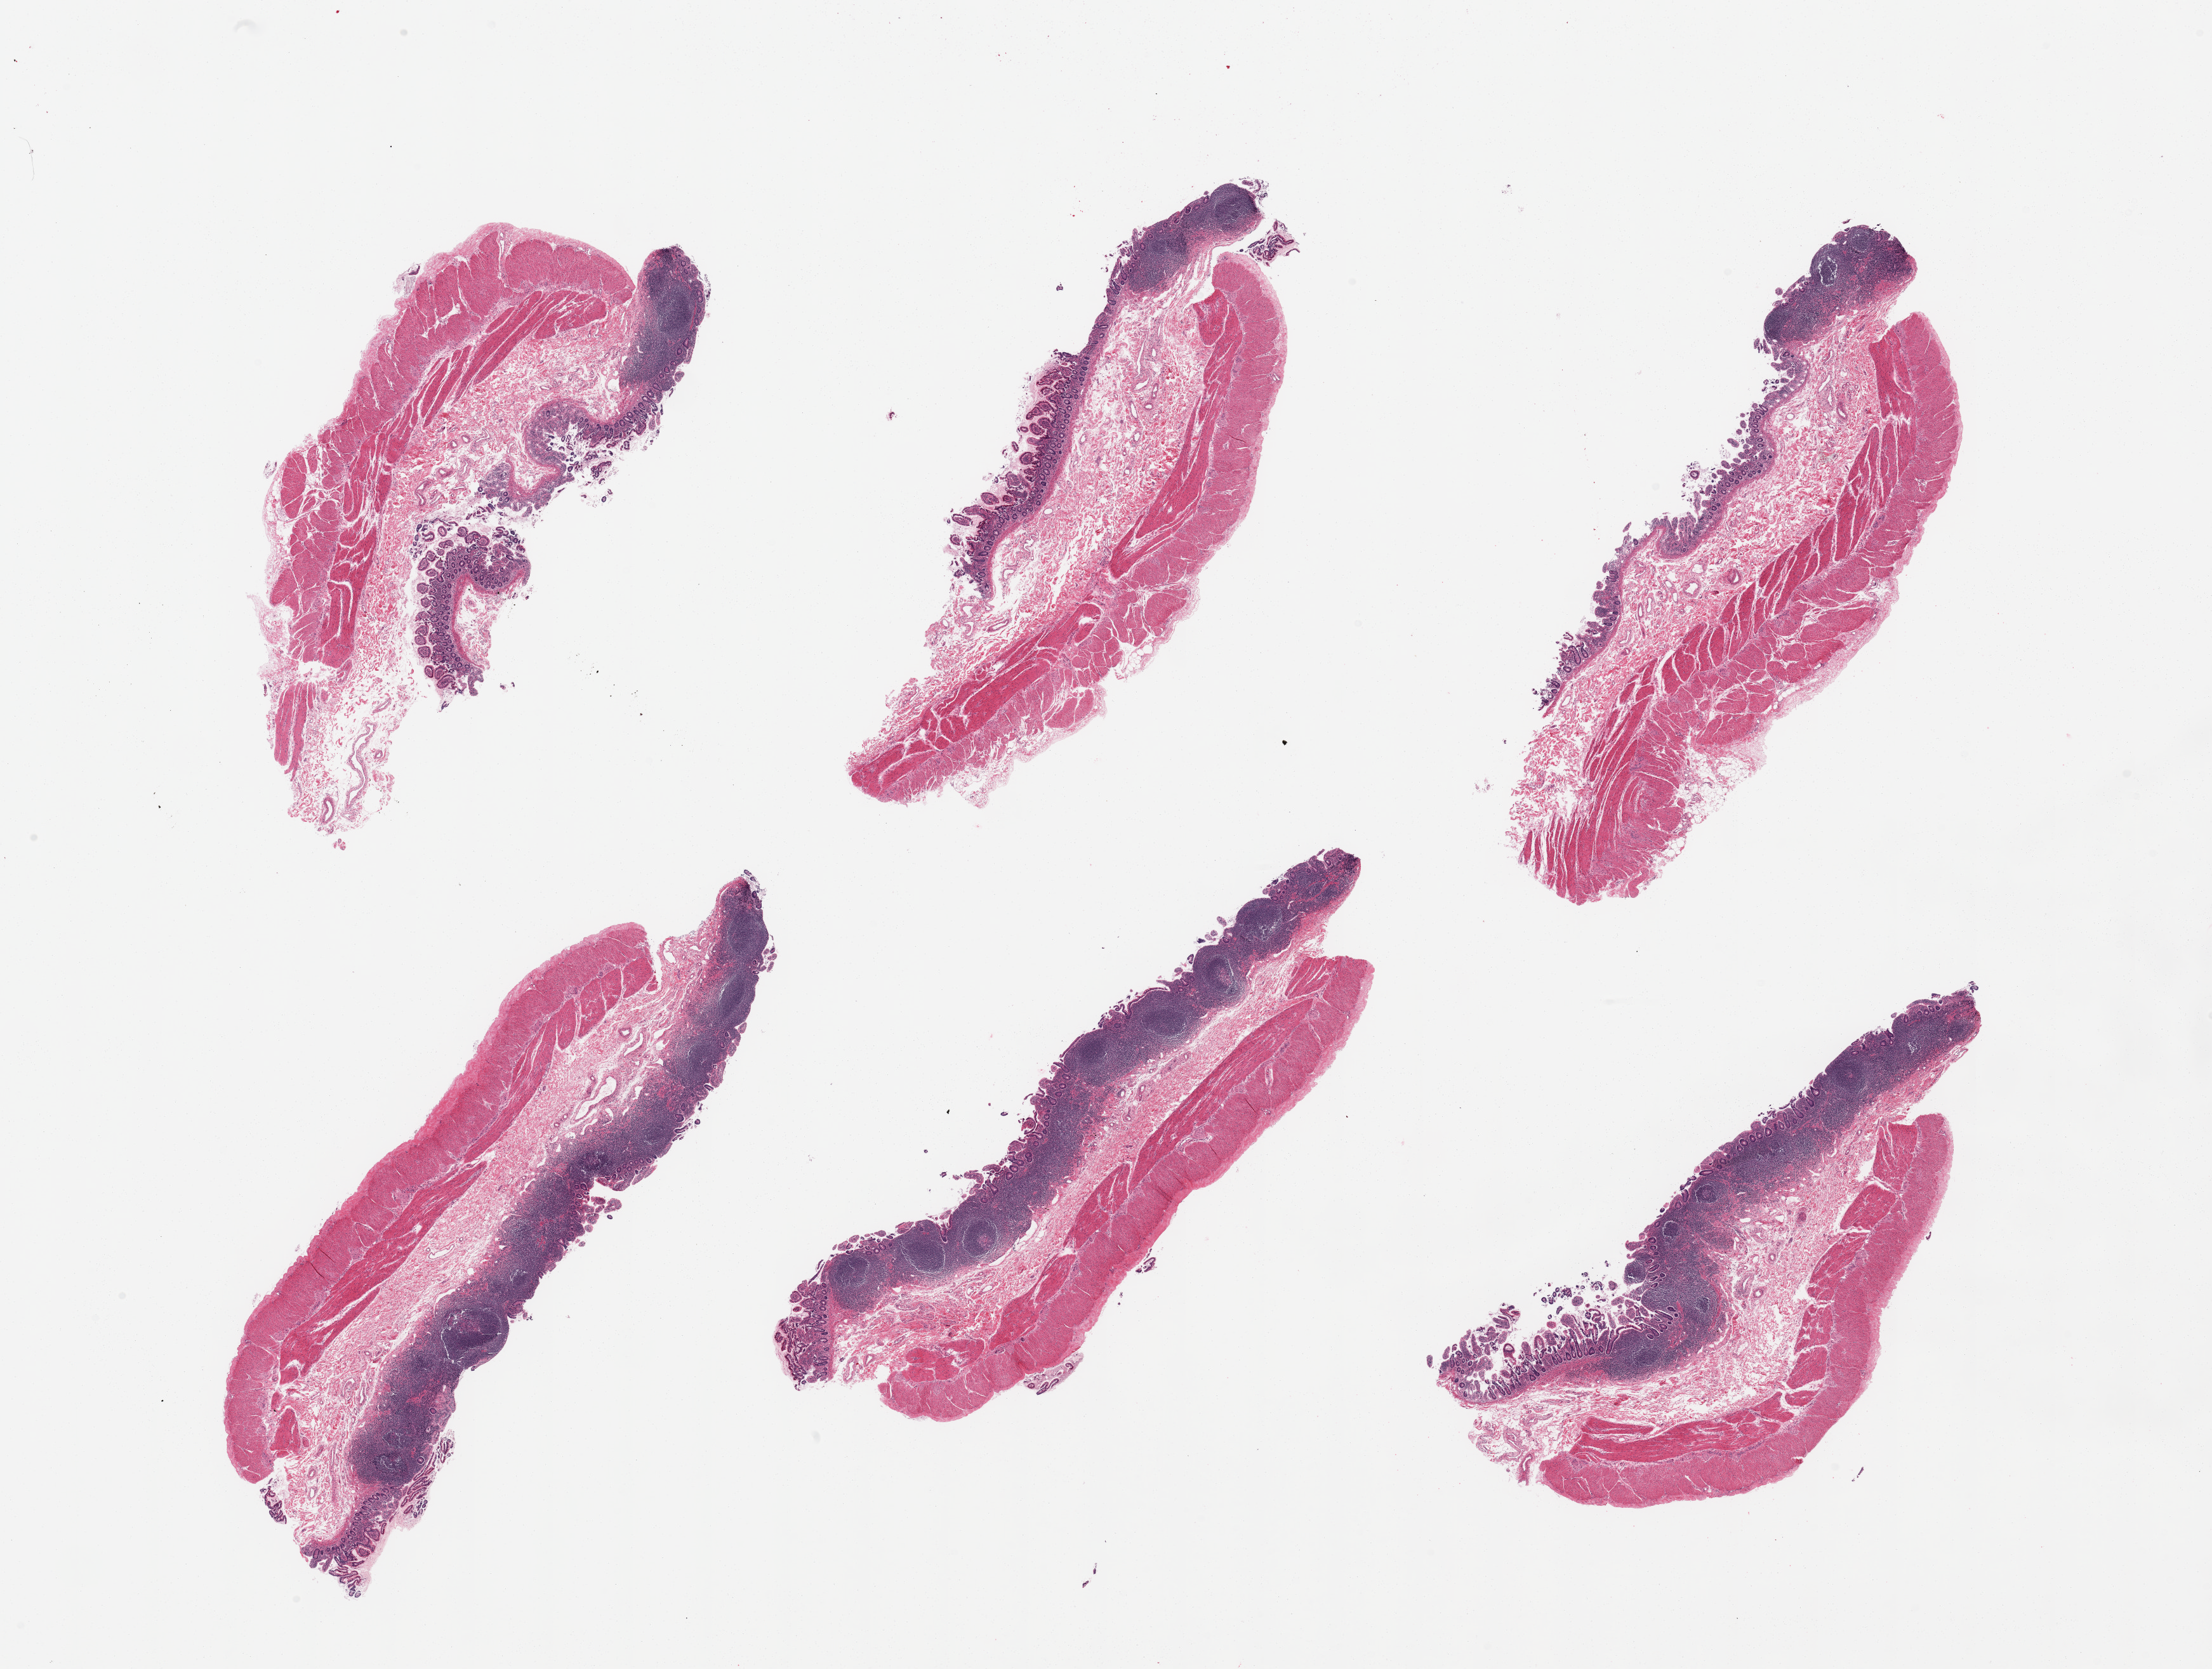
H&E whole-slide image, low-resolution overview of the scanned area, about 27.6 x 20.8 mm. Donor: female.
* specimen: PAXgene-fixed paraffin-embedded (PFPE) section; section of ileum (target tissue); donor tissue sample